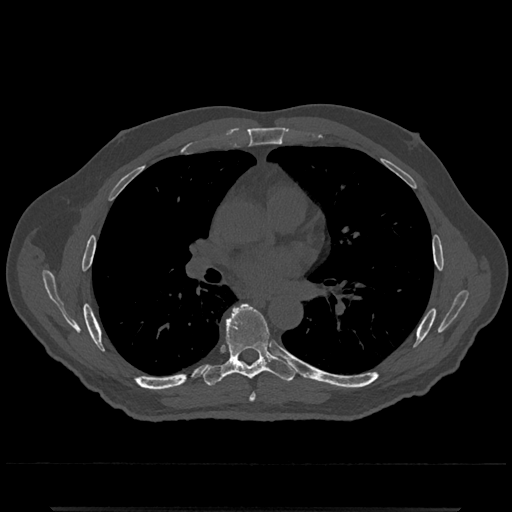
CT including the spine, one axial slice; slice 729 of 797 in the series (ordered by position); reconstruction kernel Br40s/3; bone window (W 1800 / L 400 HU); 512 × 512 image matrix. Patient: male, 67 years. Case-level facts recorded for this patient, not image findings: primary cancer: prostate.
Annotated regions visible in this slice (semi-automatically segmented with operator editing):
- T6 vertebra: bounding box <249,394,256,402> (left, top, right, bottom; pixels)
- T7 vertebra: <204,304,297,386>